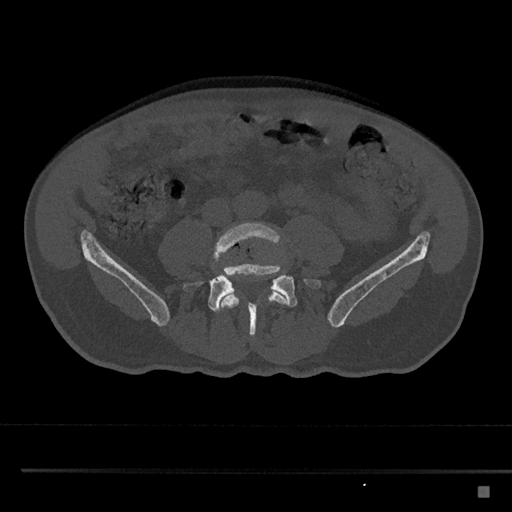
CT including the spine, one axial slice; position 604 of 797 along the scan axis; reconstruction kernel Br40s/3; 120 kVp; bone window (W 1800 / L 400 HU); 0.5 mm slice thickness; 512 × 512 image matrix, field of view 391 × 391 mm. Male patient, age 59 years. Case-level facts recorded for this patient, not image findings: primary cancer: prostate.
Structures marked on this image (semi-automatic segmentation, software-assisted and operator-edited):
- L4 vertebra: bounding box <212,222,289,320> (left, top, right, bottom; pixels)
- L5 vertebra: <181,261,322,338>